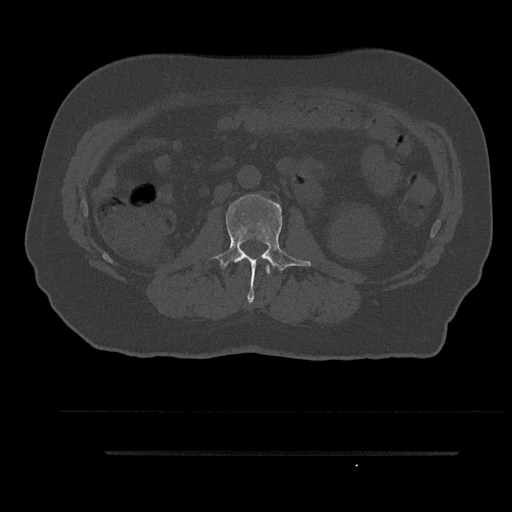
CT including the spine, one axial slice; position 110 of 797 along the scan axis; 120 kVp; bone window (W 1800 / L 400 HU); 0.5 mm slice thickness; 512 × 512 image matrix, field of view 432 × 432 mm. Patient: male, 63 years. From the clinical record (not read from this slice): primary cancer: renal; vertebrae with lytic lesions (as recorded): T8.
Outlined on this slice (semi-automatic segmentation, software-assisted and operator-edited):
- L1 vertebra: bounding box (x1, y1, x2, y2) in pixels: (265, 265, 270, 274)
- L2 vertebra: (210, 195, 311, 302)